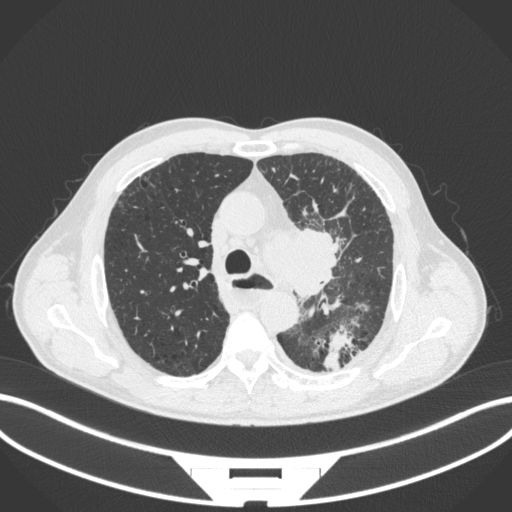
Chest CT, one axial slice; slice 265 of 411 in the series (ordered by position); lung window (W 1500 / L -600 HU); 1 mm slice thickness; 512 × 512 image matrix. Patient: male, 57 years. Case-level facts recorded for this patient, not image findings: clinical TNM (as recorded): T2a N1 M0.
Outlined on this slice (bounding box drawn by a radiologist):
- lung tumour (recorded histology: squamous cell carcinoma): bounding box <251,219,348,301> (left, top, right, bottom; pixels)